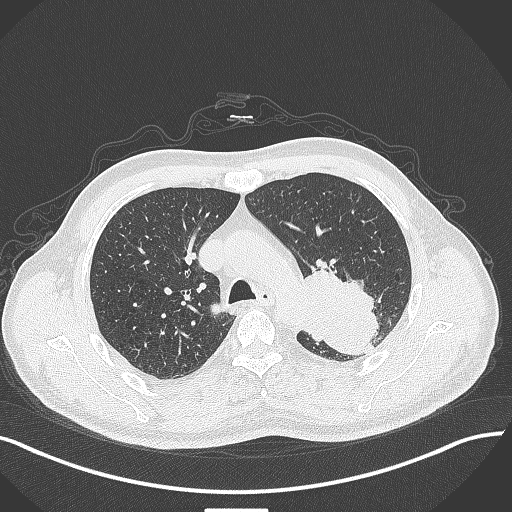
Chest CT, one axial slice; position 302 of 429 along the scan axis; reconstruction kernel B70f; 120 kVp; lung window (W 1500 / L -600 HU); 1 mm slice thickness; 512 × 512 image matrix, field of view 400 × 400 mm. Patient: male, 55 years. Case-level facts recorded for this patient, not image findings: clinical TNM (as recorded): T3 N0 M1c; histopathological grade: G3.
Annotated regions visible in this slice (rectangle marked by the reading radiologist):
- lung tumour (recorded histology: adenocarcinoma): box from (x=298, y=271) to (x=384, y=361) px